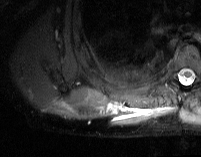
MRI of an extremity soft-tissue mass, one axial slice. Slice 14 of 74 in the series (ordered by position). STIR. MR volume resampled by the dataset authors to the PET/CT grid (not the native acquisition matrix). 3.27 mm slice thickness. 201 × 157 image matrix. Male patient. Case-level facts recorded for this patient, not image findings: histological type: pleiomorphic spindle cell undifferentiated; grade: high; site of the primary tumour: right parascapusular.
Annotated regions visible in this slice (expert contour drawn on MRI and transferred to this co-registered scan by the dataset authors):
- gross tumour volume including surrounding oedema: bounding box (x1, y1, x2, y2) in pixels: (103, 100, 173, 124)